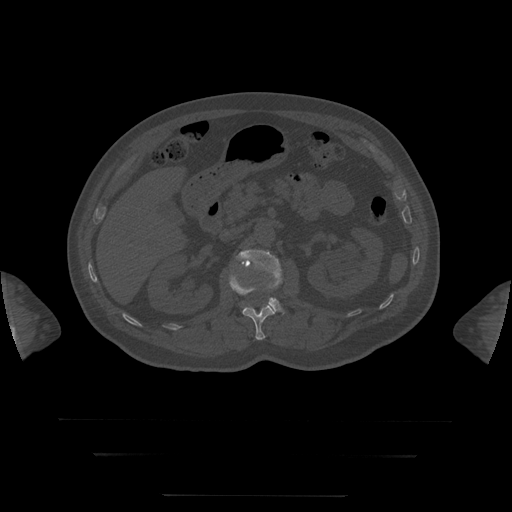
CT including the spine, one axial slice. Position 38 of 397 along the scan axis. Reconstruction kernel STANDARD. 120 kVp. Bone window (W 1800 / L 400 HU). 512 × 512 image matrix, field of view 510 × 510 mm. Patient age 73 years. Case-level facts recorded for this patient, not image findings: primary cancer: prostate.
Annotated regions visible in this slice (semi-automatic segmentation, software-assisted and operator-edited):
- L1 vertebra: bounding box (x1, y1, x2, y2) in pixels: (229, 274, 275, 340)